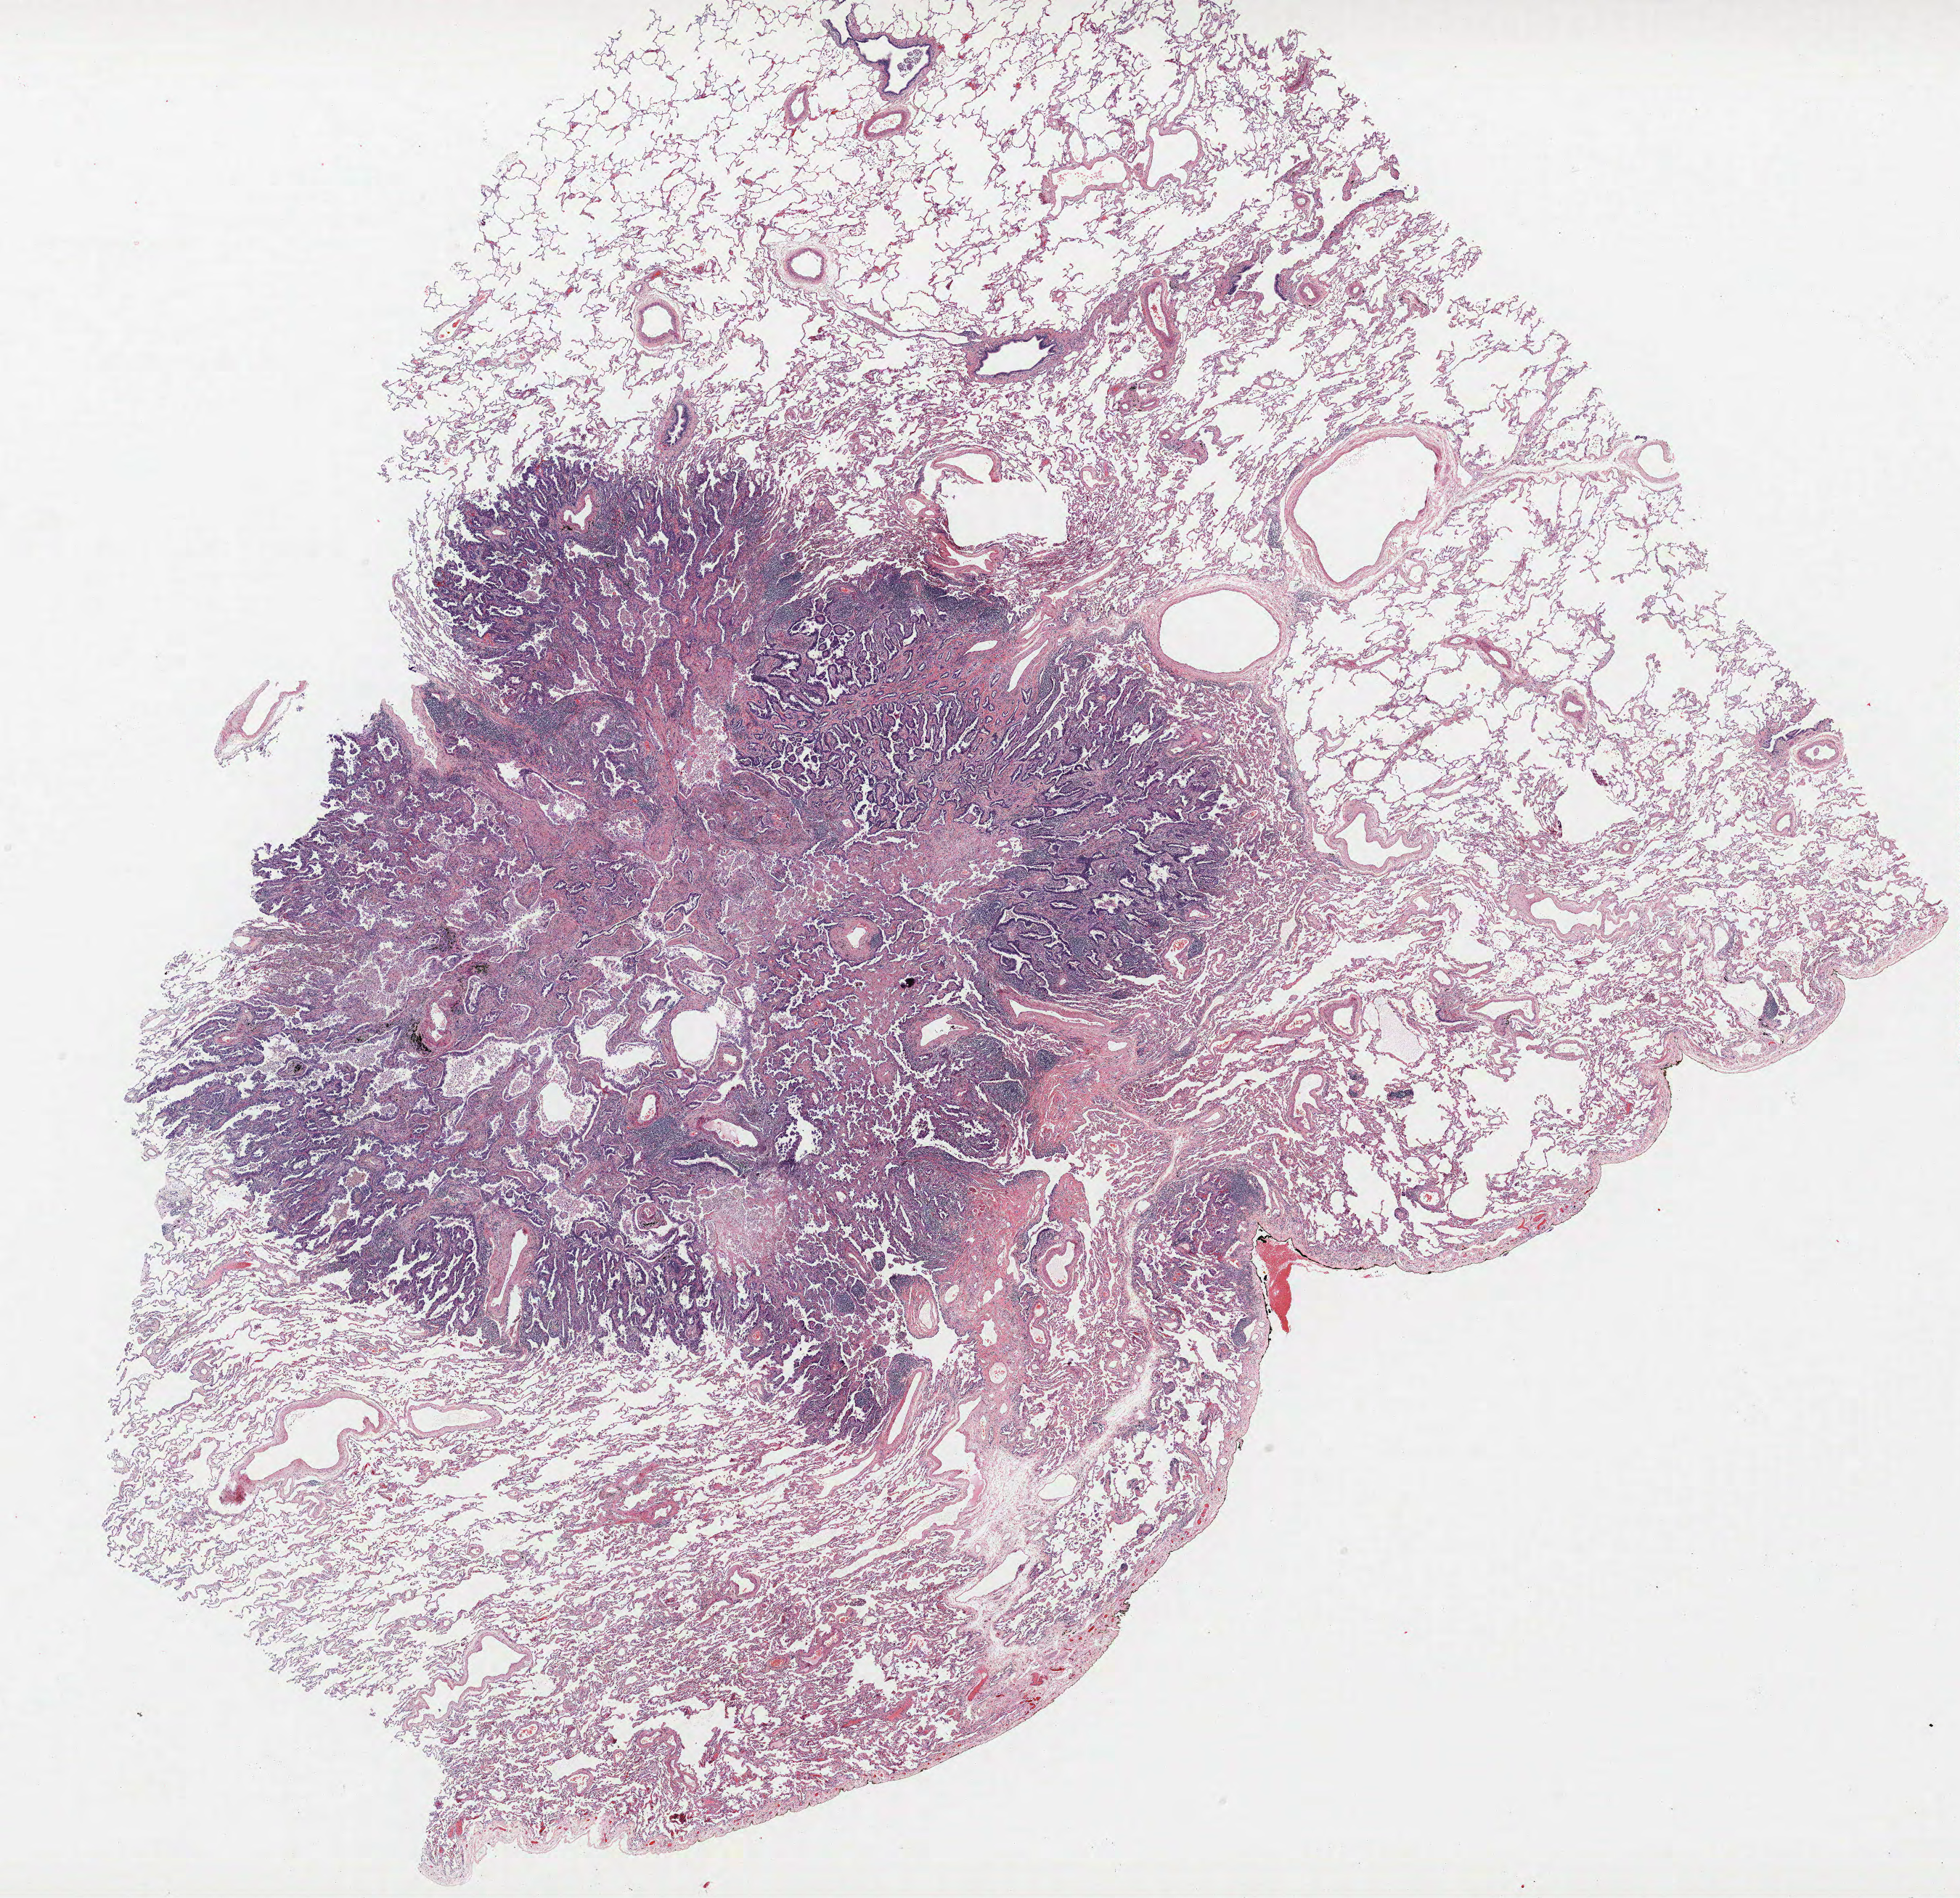
Whole-slide histology image, H&E — whole scanned area (about 21.6 x 20.9 mm, acquisition: 40x scan) shown as a low-resolution overview, FFPE section, lung. Female patient, aged 59 at enrolment. Grade: poorly differentiated (G3).
Primary tumour location (clinical record): left lower lobe. Participant's lung-cancer diagnosis: Adenocarcinoma, NOS. Stage (AJCC 6th edition): IA. Tumour size (pathology): 22 mm.